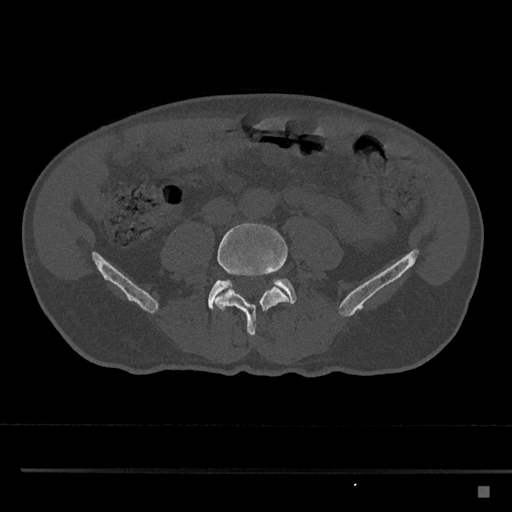
CT including the spine, one axial slice; position 618 of 797 along the scan axis; reconstruction kernel Br40s/3; bone window (W 1800 / L 400 HU); 0.5 mm slice thickness; 512 × 512 image matrix, field of view 391 × 391 mm. Male patient, age 59 years. Case-level facts recorded for this patient, not image findings: primary cancer: prostate.
Outlined on this slice (semi-automatically segmented with operator editing):
- L4 vertebra: box from (x=215, y=223) to (x=290, y=336) px
- L5 vertebra: (x=208, y=278)–(x=297, y=310)